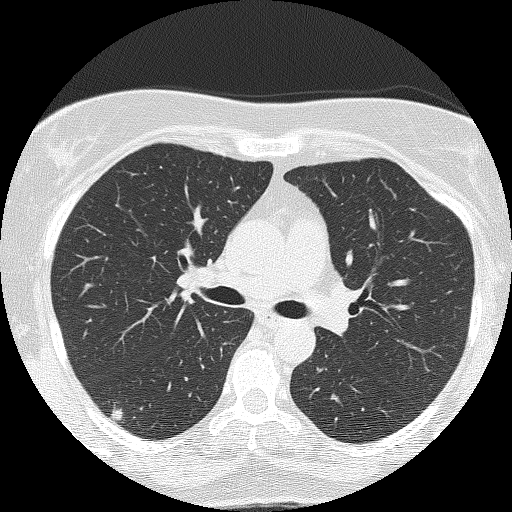
Low-dose screening chest CT, one axial slice; position 87 of 143 along the scan axis; 120 kVp; lung window (W 1500 / L -600 HU); 2 mm slice thickness; 512 × 512 image matrix, field of view 301 × 301 mm.
Annotated regions visible in this slice (expert manual segmentation):
- lesion 1 (tumor, lower lobe of right lung): bounding box <112,409,123,420> (left, top, right, bottom; pixels)